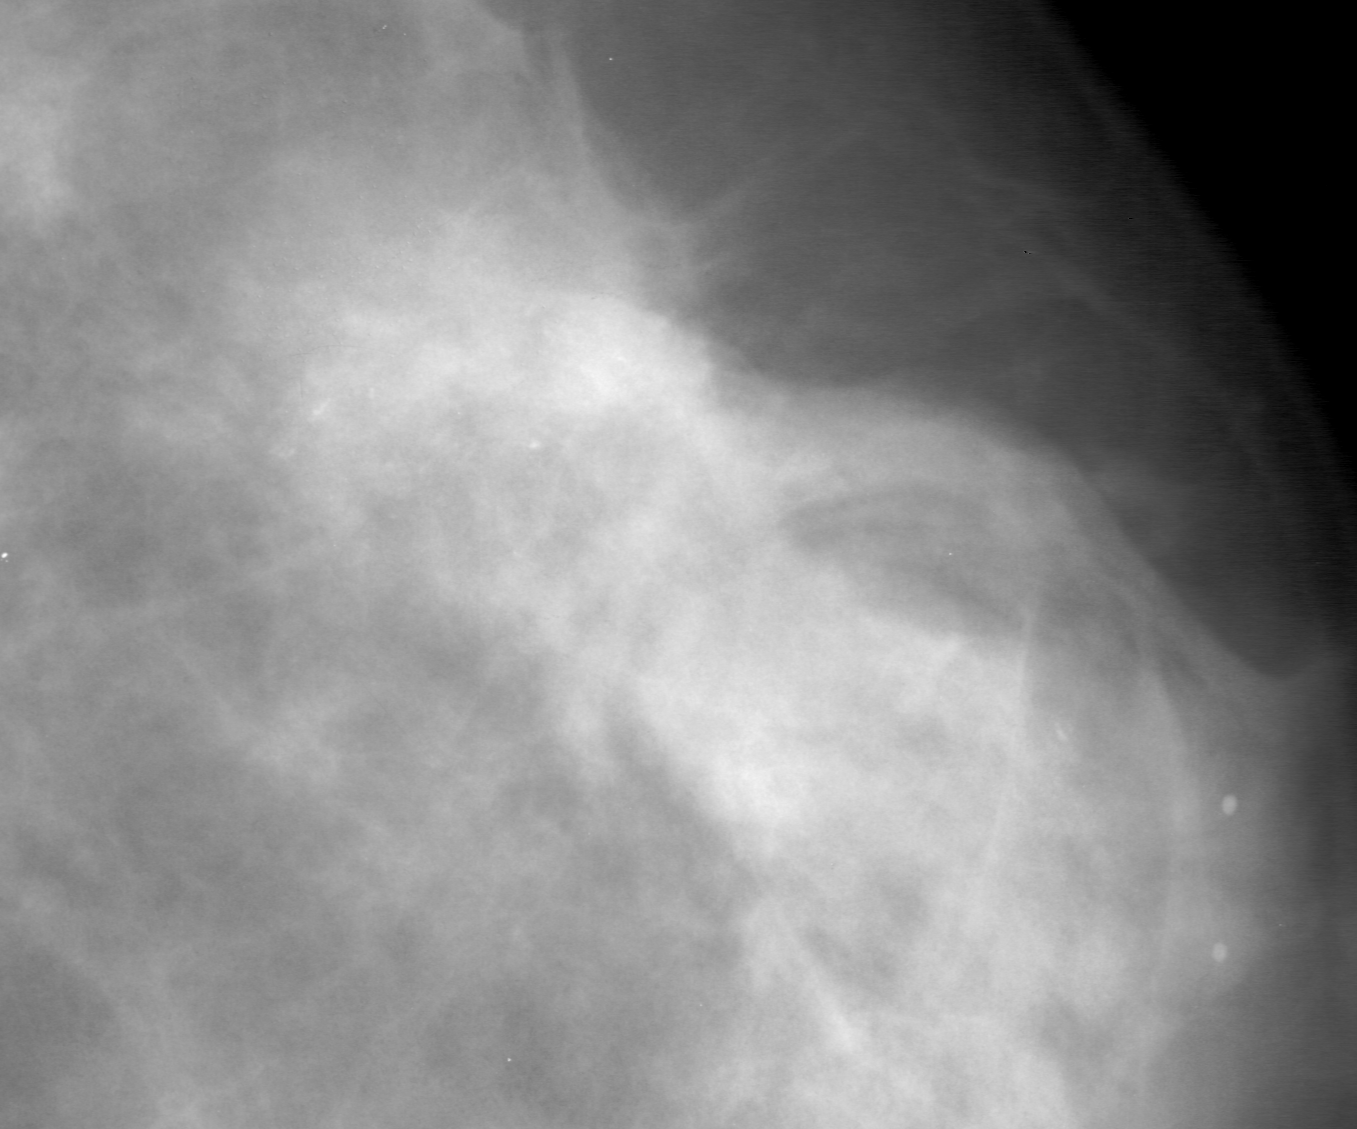
Region of interest cut from a scanned film mammogram (one marked finding), left breast, CC view.
- Finding: calcifications, morphology amorphous, distribution segmental; BI-RADS assessment category 4; pathology (as recorded): malignant.